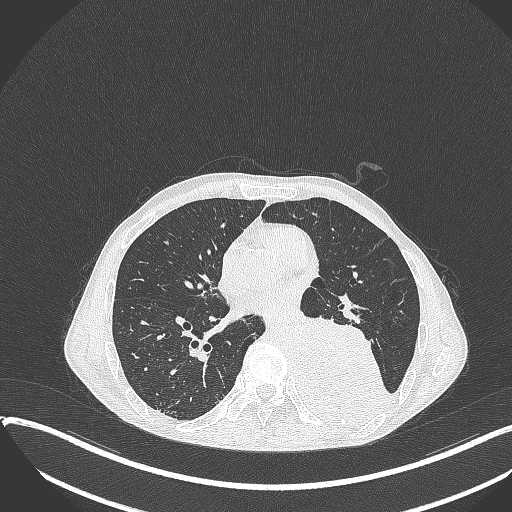
Chest CT, one axial slice. Slice 167 of 401 in the series (ordered by position). Reconstruction kernel B70f. Lung window (W 1500 / L -600 HU). 1 mm slice thickness. 512 × 512 image matrix, field of view 400 × 400 mm. Male patient, age 57 years. From the clinical record (not read from this slice): clinical TNM (as recorded): T4 N0 M0.
Annotated regions visible in this slice (bounding box drawn by a radiologist):
- lung tumour (recorded histology: squamous cell carcinoma): bounding box [x1, y1, x2, y2] px = [295, 307, 398, 427]